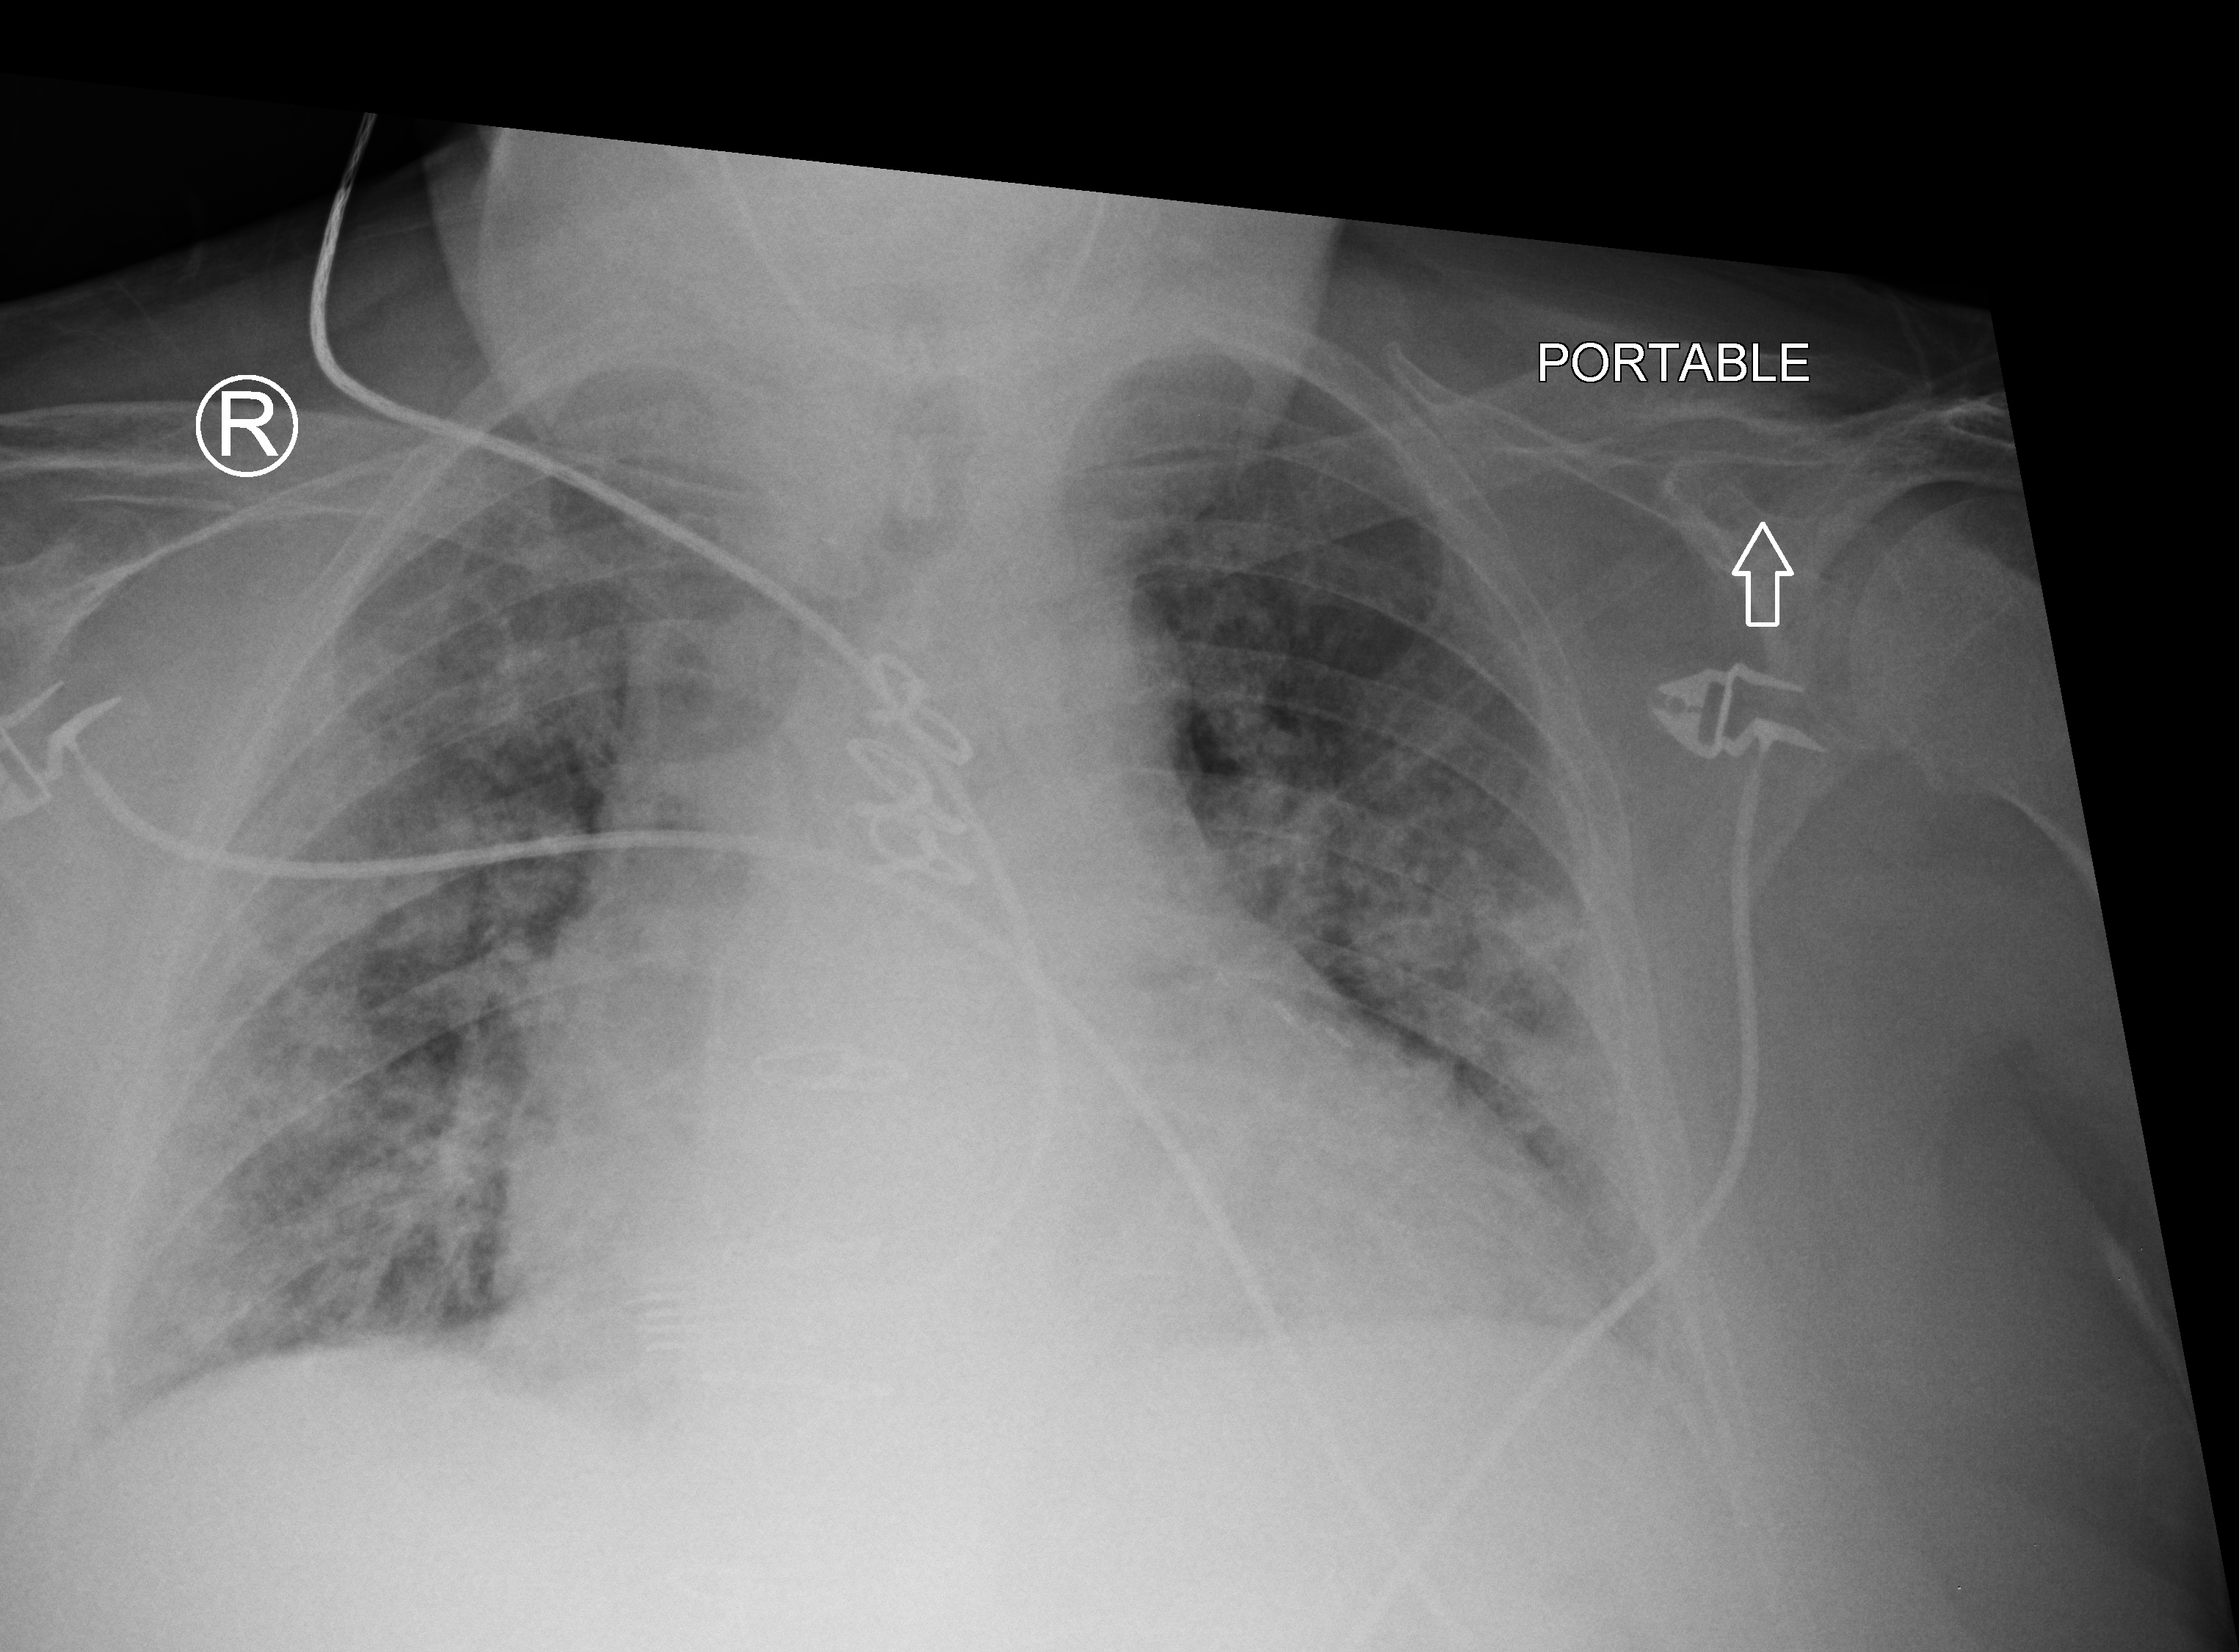
Bedside chest radiograph (computed radiography), anteroposterior (AP) projection. Male patient hospitalised with COVID-19, age 75–90 years.
From the hospital-stay record, not from the radiograph (when in the stay this image was taken is not recorded):
- diabetes (admission record): no